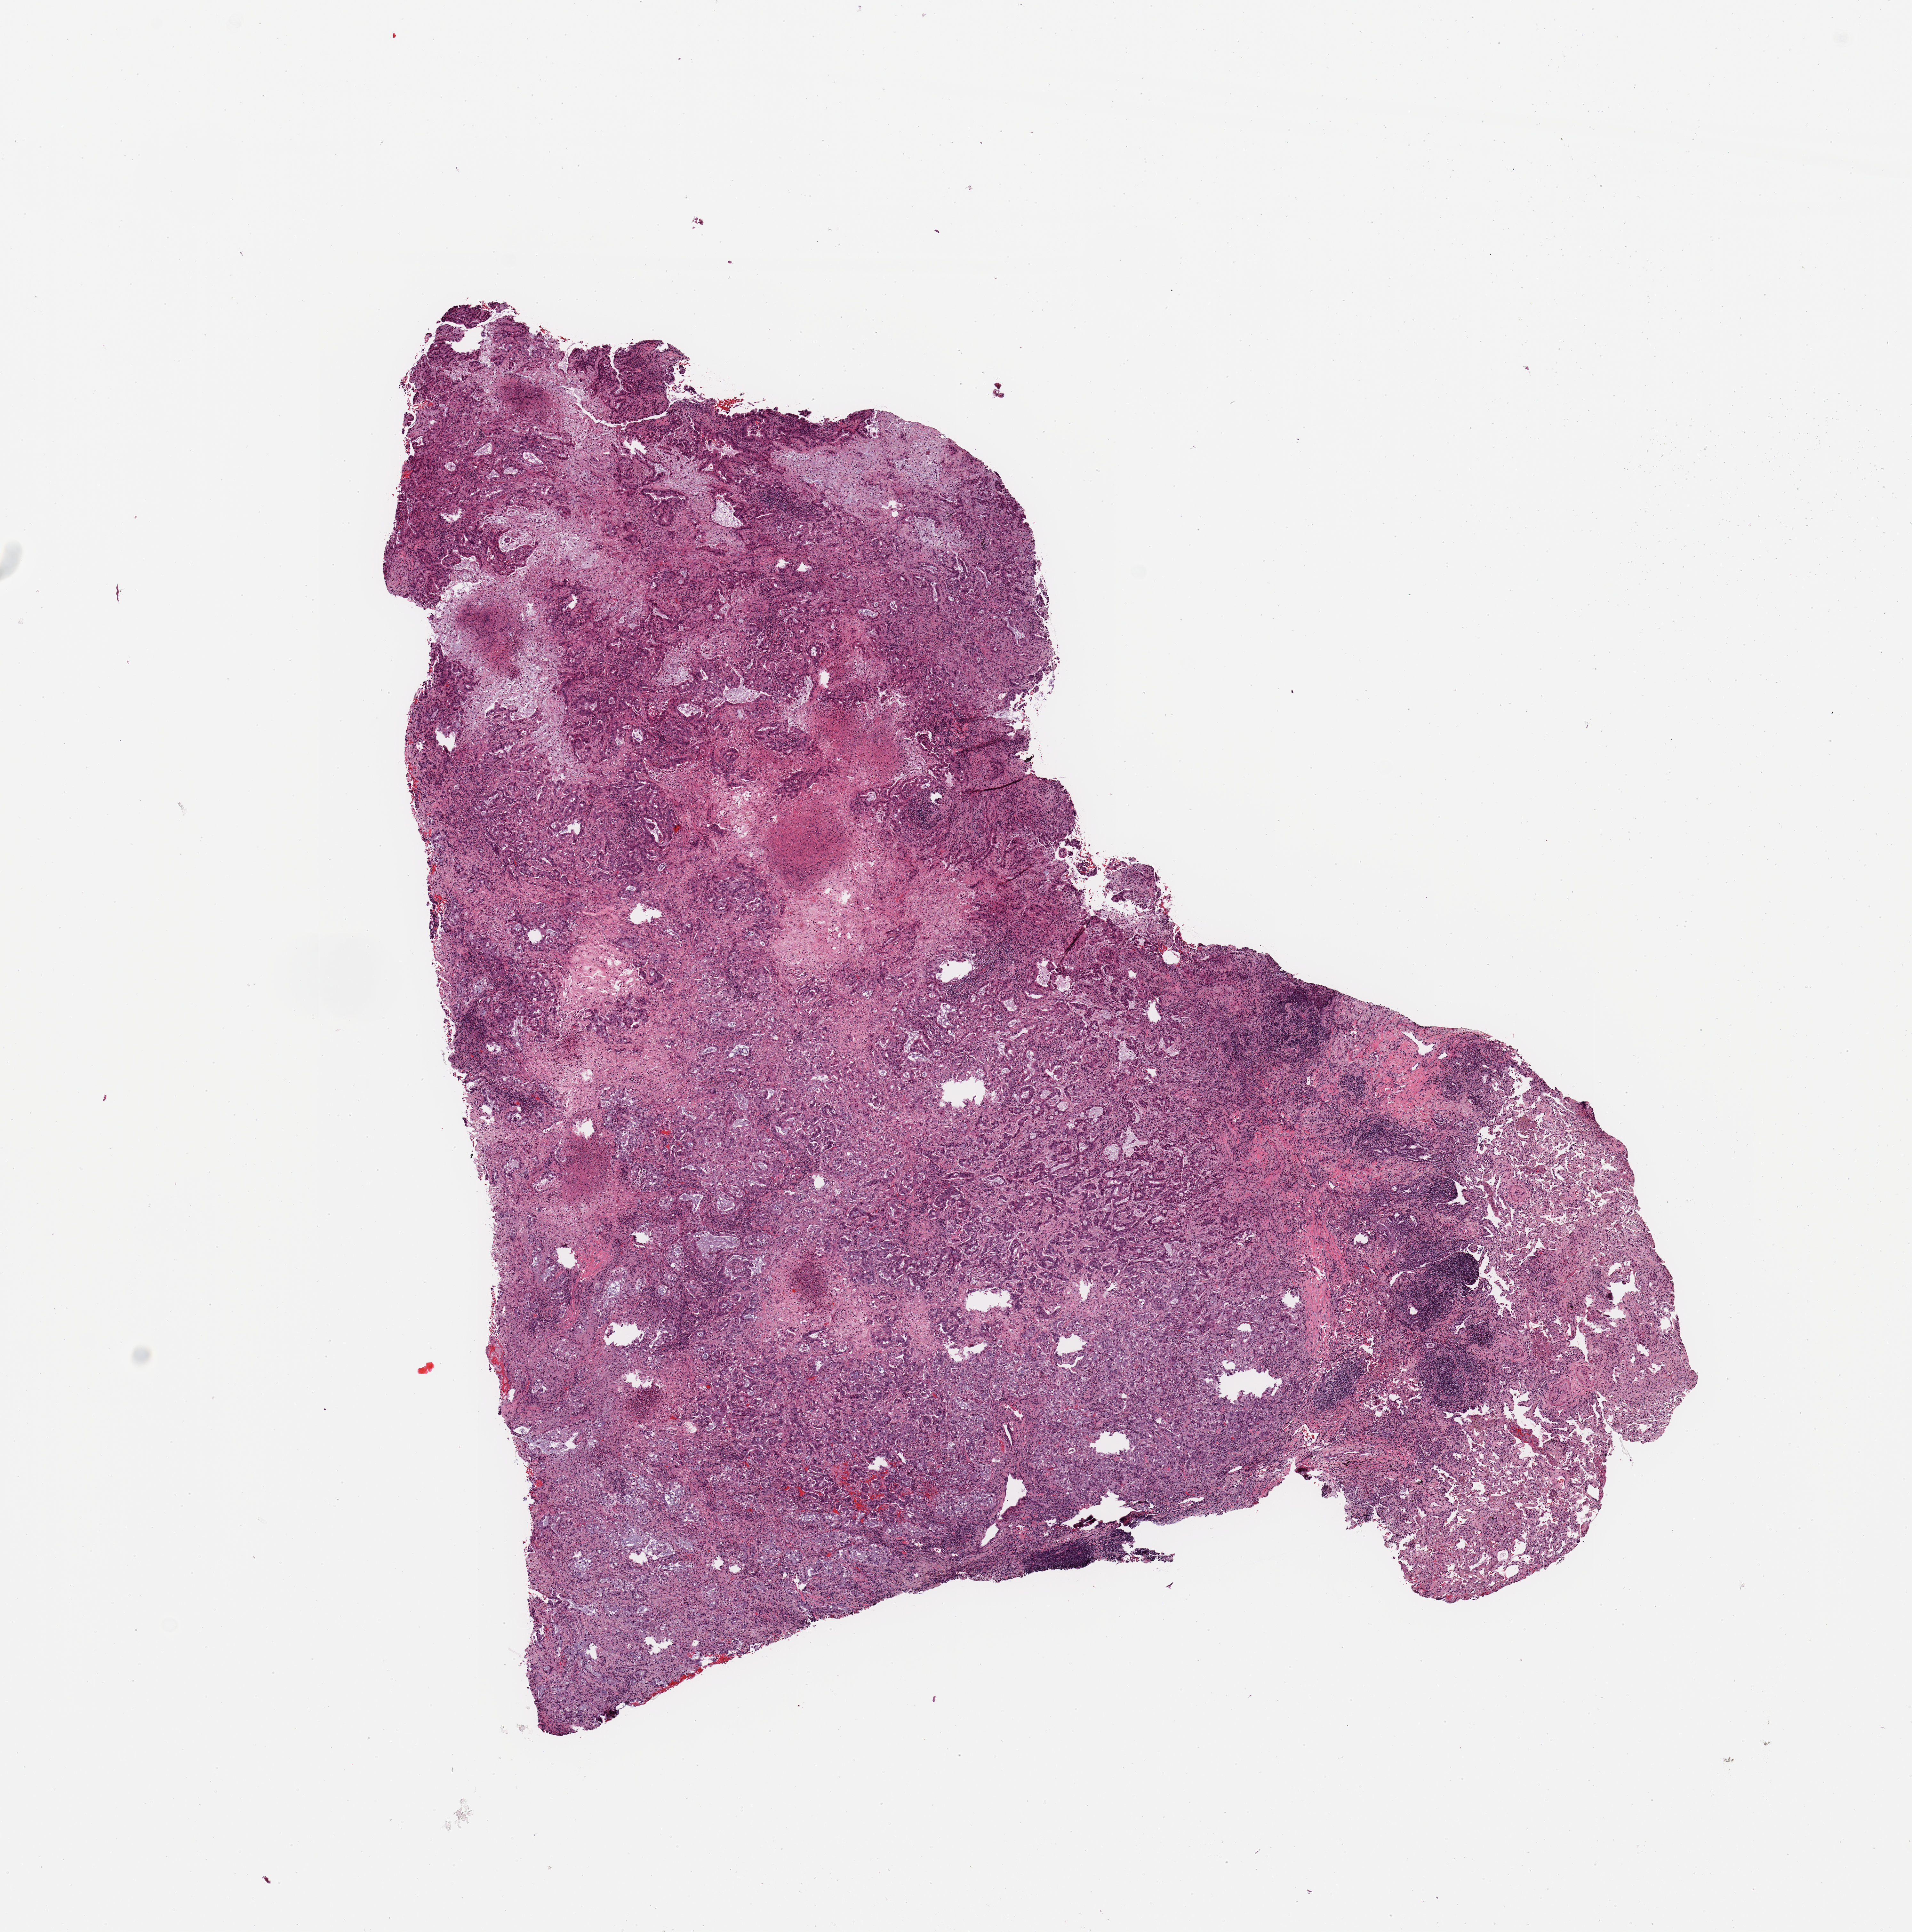
Whole-slide histology image, H&E, whole scanned area (about 11.8 x 11.9 mm, slide scanned at 20x) shown as a low-resolution overview, lung, tumour tissue. Female, 61 y/o. Histologic grade: G2 (moderately differentiated).
Primary tumour site (as recorded): right upper lobe. Diagnosis: Adenocarcinoma, NOS. AJCC pathologic stage: IB.